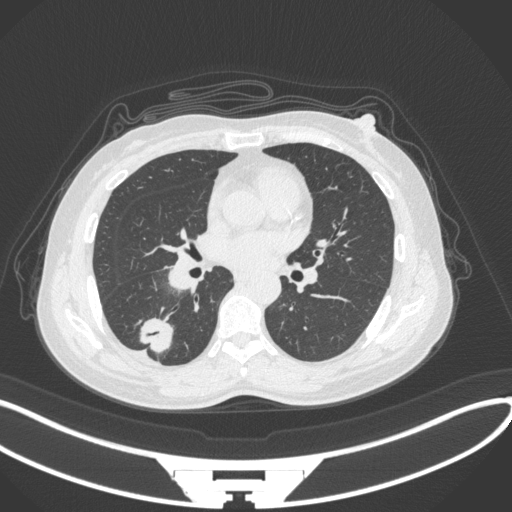
Chest CT, one axial slice; slice 150 of 352 in the series (ordered by position); lung window (W 1500 / L -600 HU); 1 mm slice thickness; 512 × 512 image matrix, field of view 400 × 400 mm. Patient: female, 55 years. From the clinical record (not read from this slice): clinical TNM (as recorded): T1c N1 M0.
Structures marked on this image (bounding box drawn by a radiologist):
- lung tumour (recorded histology: adenocarcinoma): bounding box (x1, y1, x2, y2) in pixels: (134, 311, 176, 357)